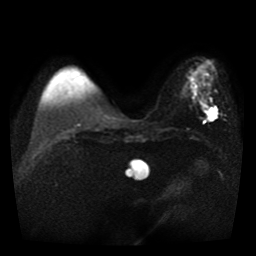
Breast MRI, one axial slice. Slice 11 of 41 in the series (ordered by position). Diffusion-weighted series; image 2 of 4 stored at this slice position (different b-values; order by instance number). 1.5 T. 5 mm slice thickness. 256 × 256 image matrix. Female patient.
Annotated regions visible in this slice (outlined manually by an expert reader):
- tumour on diffusion-weighted imaging: bounding box (x1, y1, x2, y2) in pixels: (208, 108, 217, 120)